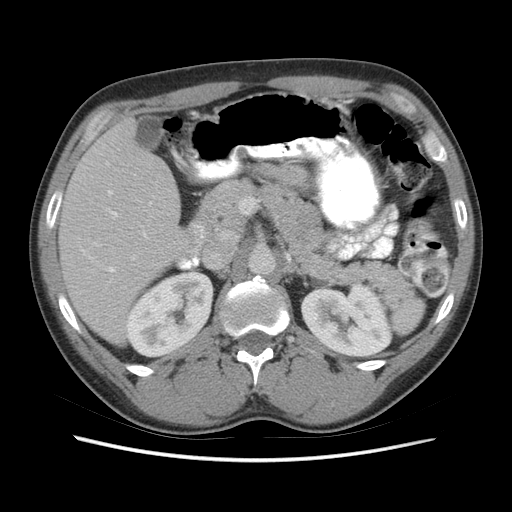
Contrast-enhanced abdominal CT (liver protocol), one axial slice. Reconstruction kernel STANDARD. 140 kVp. Soft-tissue window (W 400 / L 40 HU). 2.5 mm slice thickness. 512 × 512 image matrix, field of view 360 × 360 mm. From the clinical record (not read from this slice): diagnosis: hepatocellular carcinoma (patient treated with transarterial chemoembolisation; whether this scan precedes or follows treatment is not stated here); TNM stage (as recorded): Stage-IIIA; Child-Pugh class: A; tumour size: 6.6 cm.
Structures marked on this image (semi-automatically segmented with operator editing):
- liver parenchyma outside the tumour (the mass and vessels are separate outlines, so this box may not span the whole liver): bounding box (x1, y1, x2, y2) in pixels: (58, 118, 205, 342)
- liver vessels: (82, 162, 203, 272)